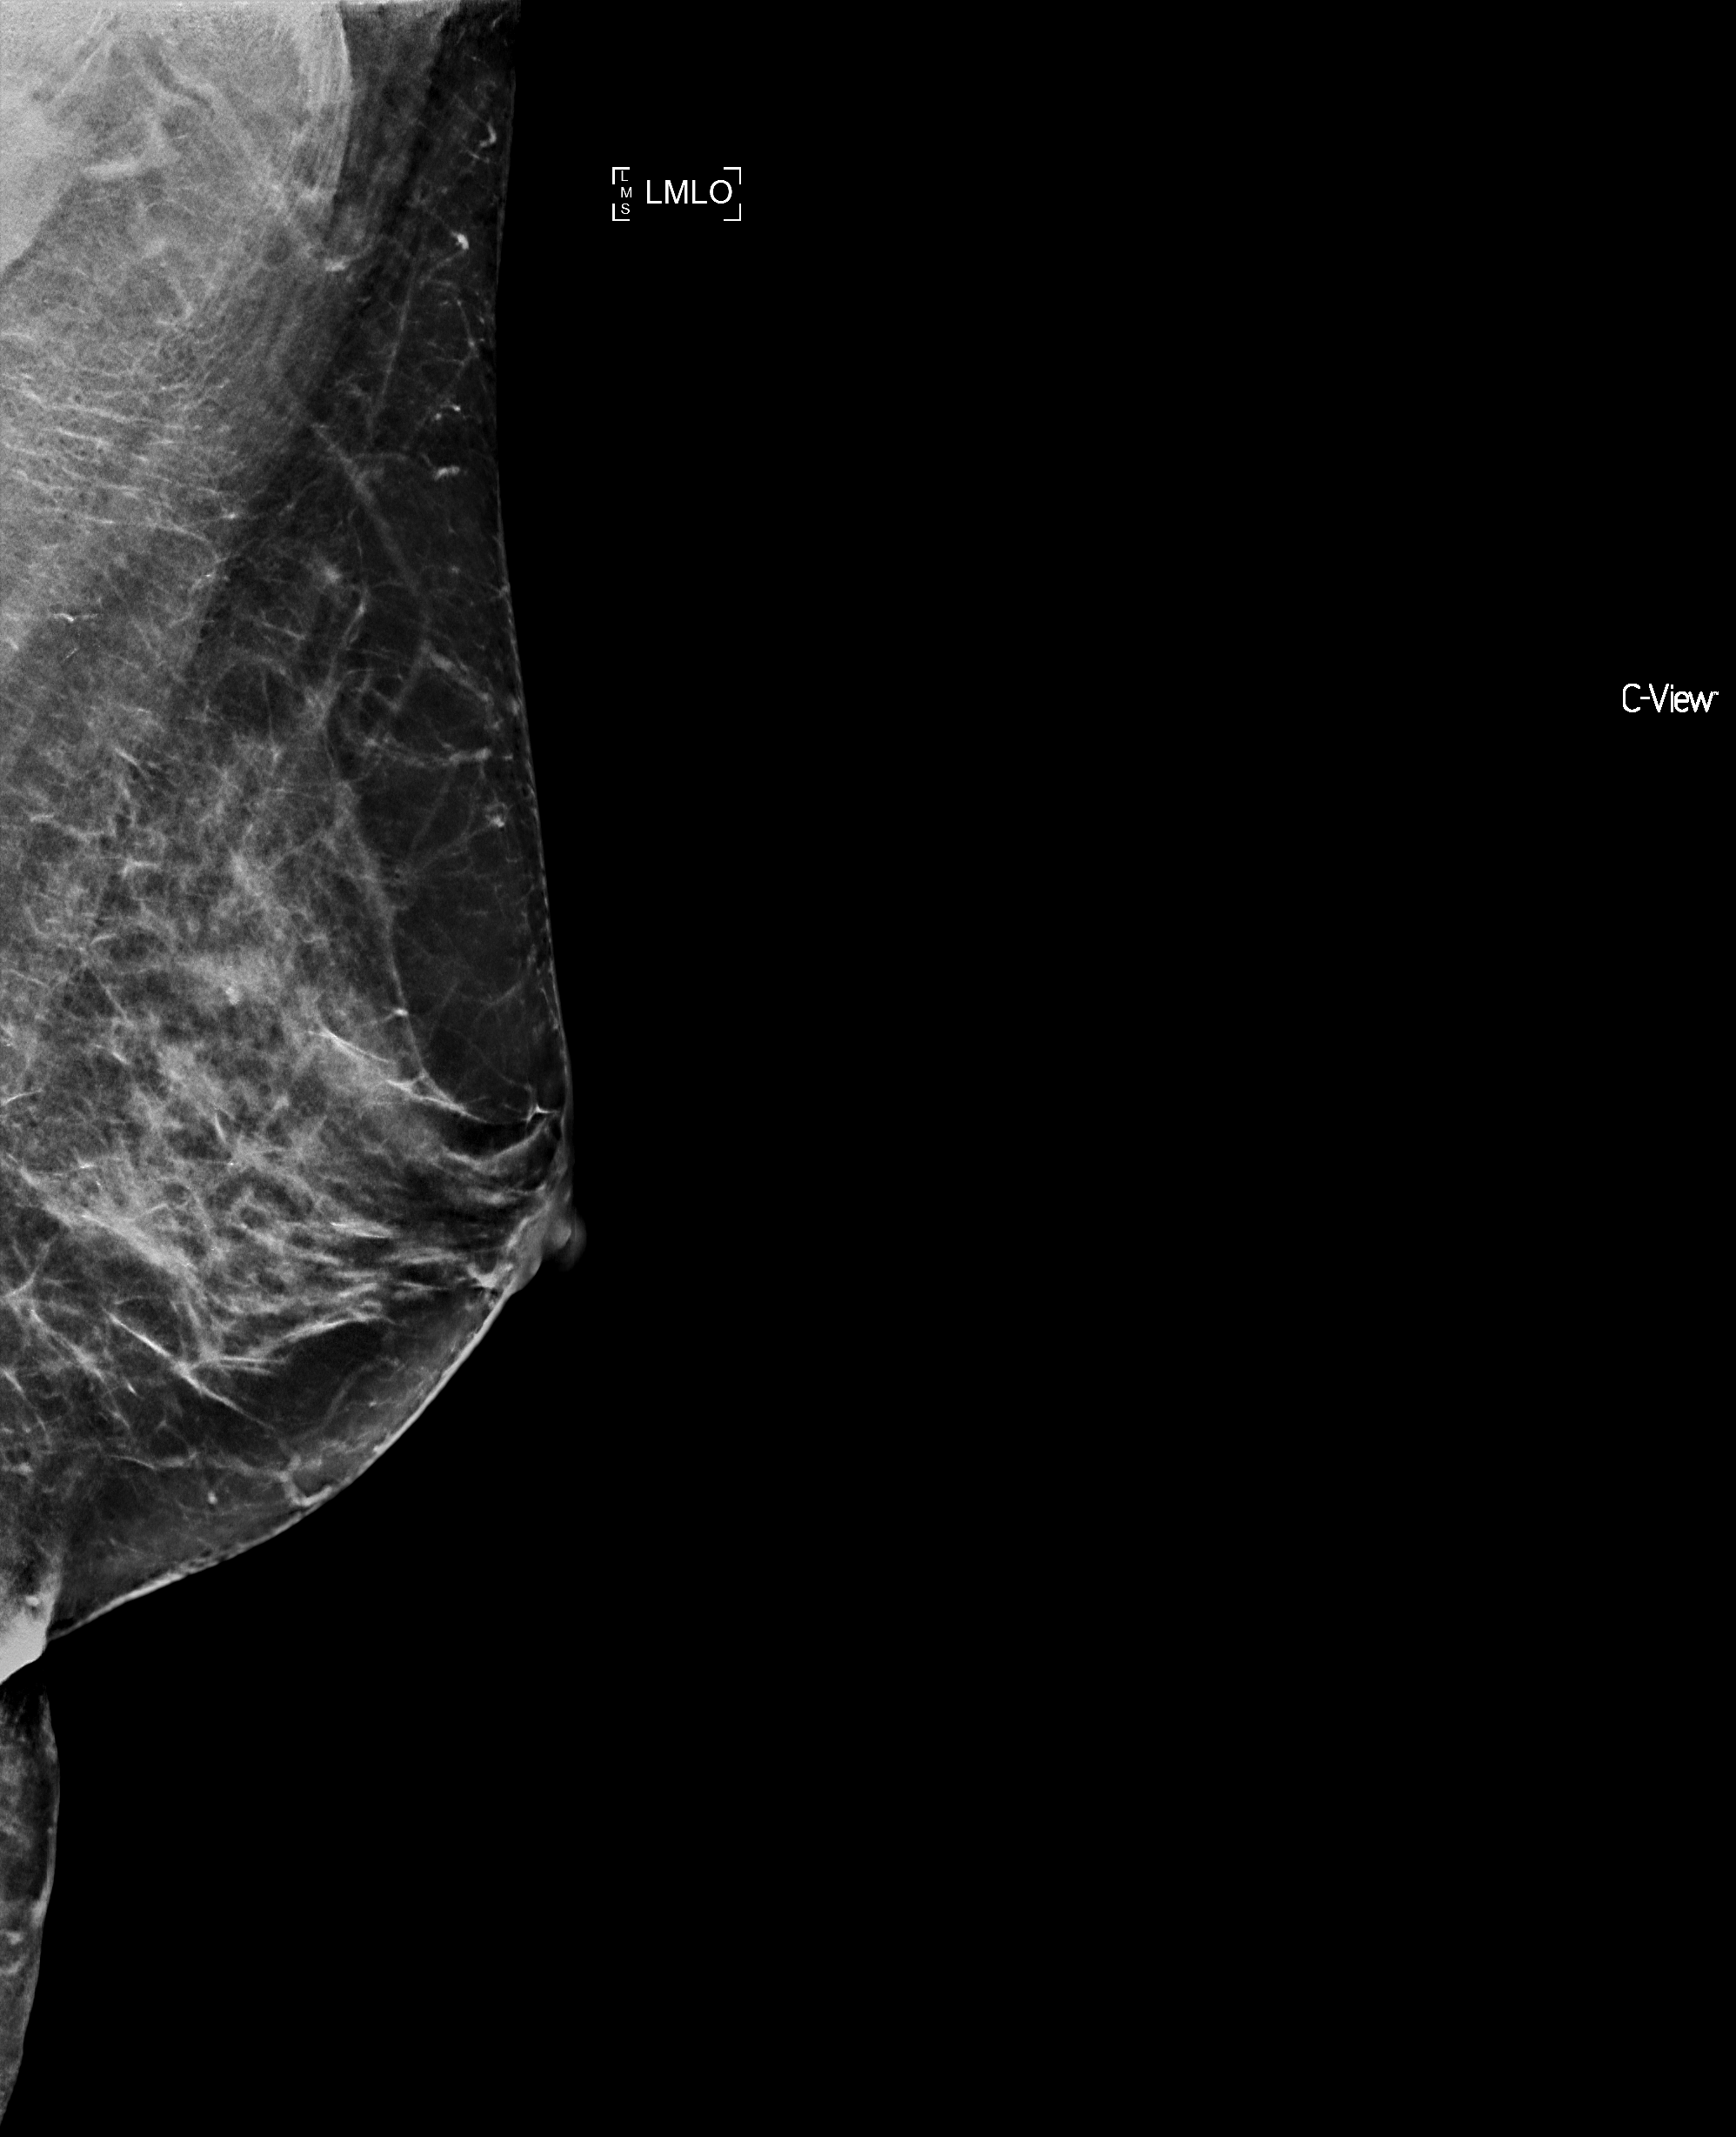
Annual screening mammography examination; compressed breast thickness 60 mm; system: Selenia Dimensions. Female patient, age 59 years.
Image type: full-field digital mammogram. Breast: left. Projection: mediolateral oblique (MLO) view. Breast density at the screening exam (both breasts): heterogeneously dense (BI-RADS density category c). Final BI-RADS category for the screening round (tomosynthesis exam, both breasts): category 1. Recall: no recall after this screen.